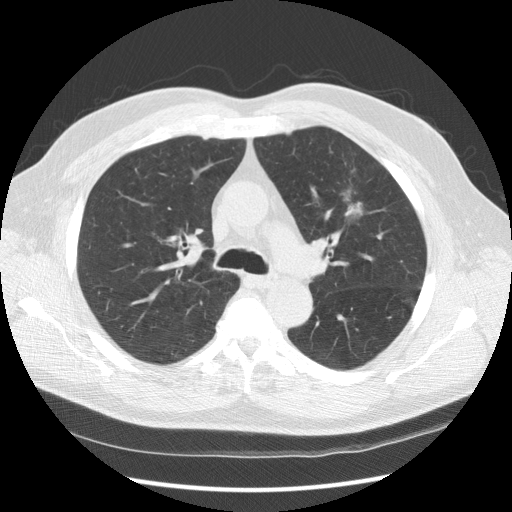
Low-dose screening chest CT, one axial slice. Slice 103 of 157 in the series (ordered by position). Reconstruction kernel STANDARD. 120 kVp. Lung window (W 1500 / L -600 HU). 2.5 mm slice thickness. 512 × 512 image matrix, field of view 370 × 370 mm.
Annotated regions visible in this slice (manually delineated by an expert):
- lesion 1 (tumor, upper lobe of left lung): bounding box <344,202,362,216> (left, top, right, bottom; pixels)